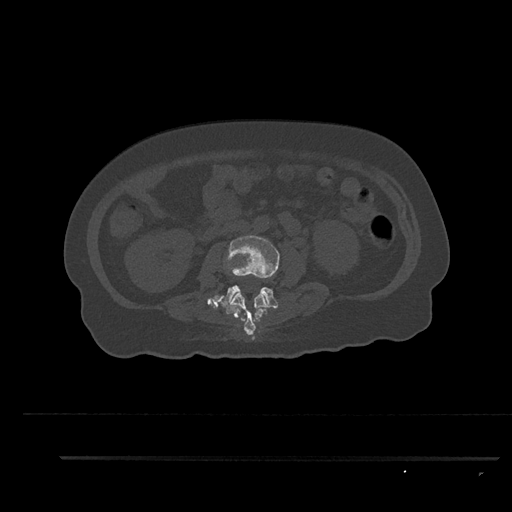
CT including the spine, one axial slice; slice 117 of 797 in the series (ordered by position); reconstruction kernel Br40s/3; 120 kVp; bone window (W 1800 / L 400 HU); 0.5 mm slice thickness; 512 × 512 image matrix, field of view 408 × 408 mm. Patient: female, 44 years. Case-level facts recorded for this patient, not image findings: primary cancer: renal; vertebrae with lytic lesions (as recorded): L1.
Outlined on this slice (semi-automatic segmentation, software-assisted and operator-edited):
- L2 vertebra: bounding box <224,293,268,335> (left, top, right, bottom; pixels)
- L3 vertebra: <218,235,280,308>